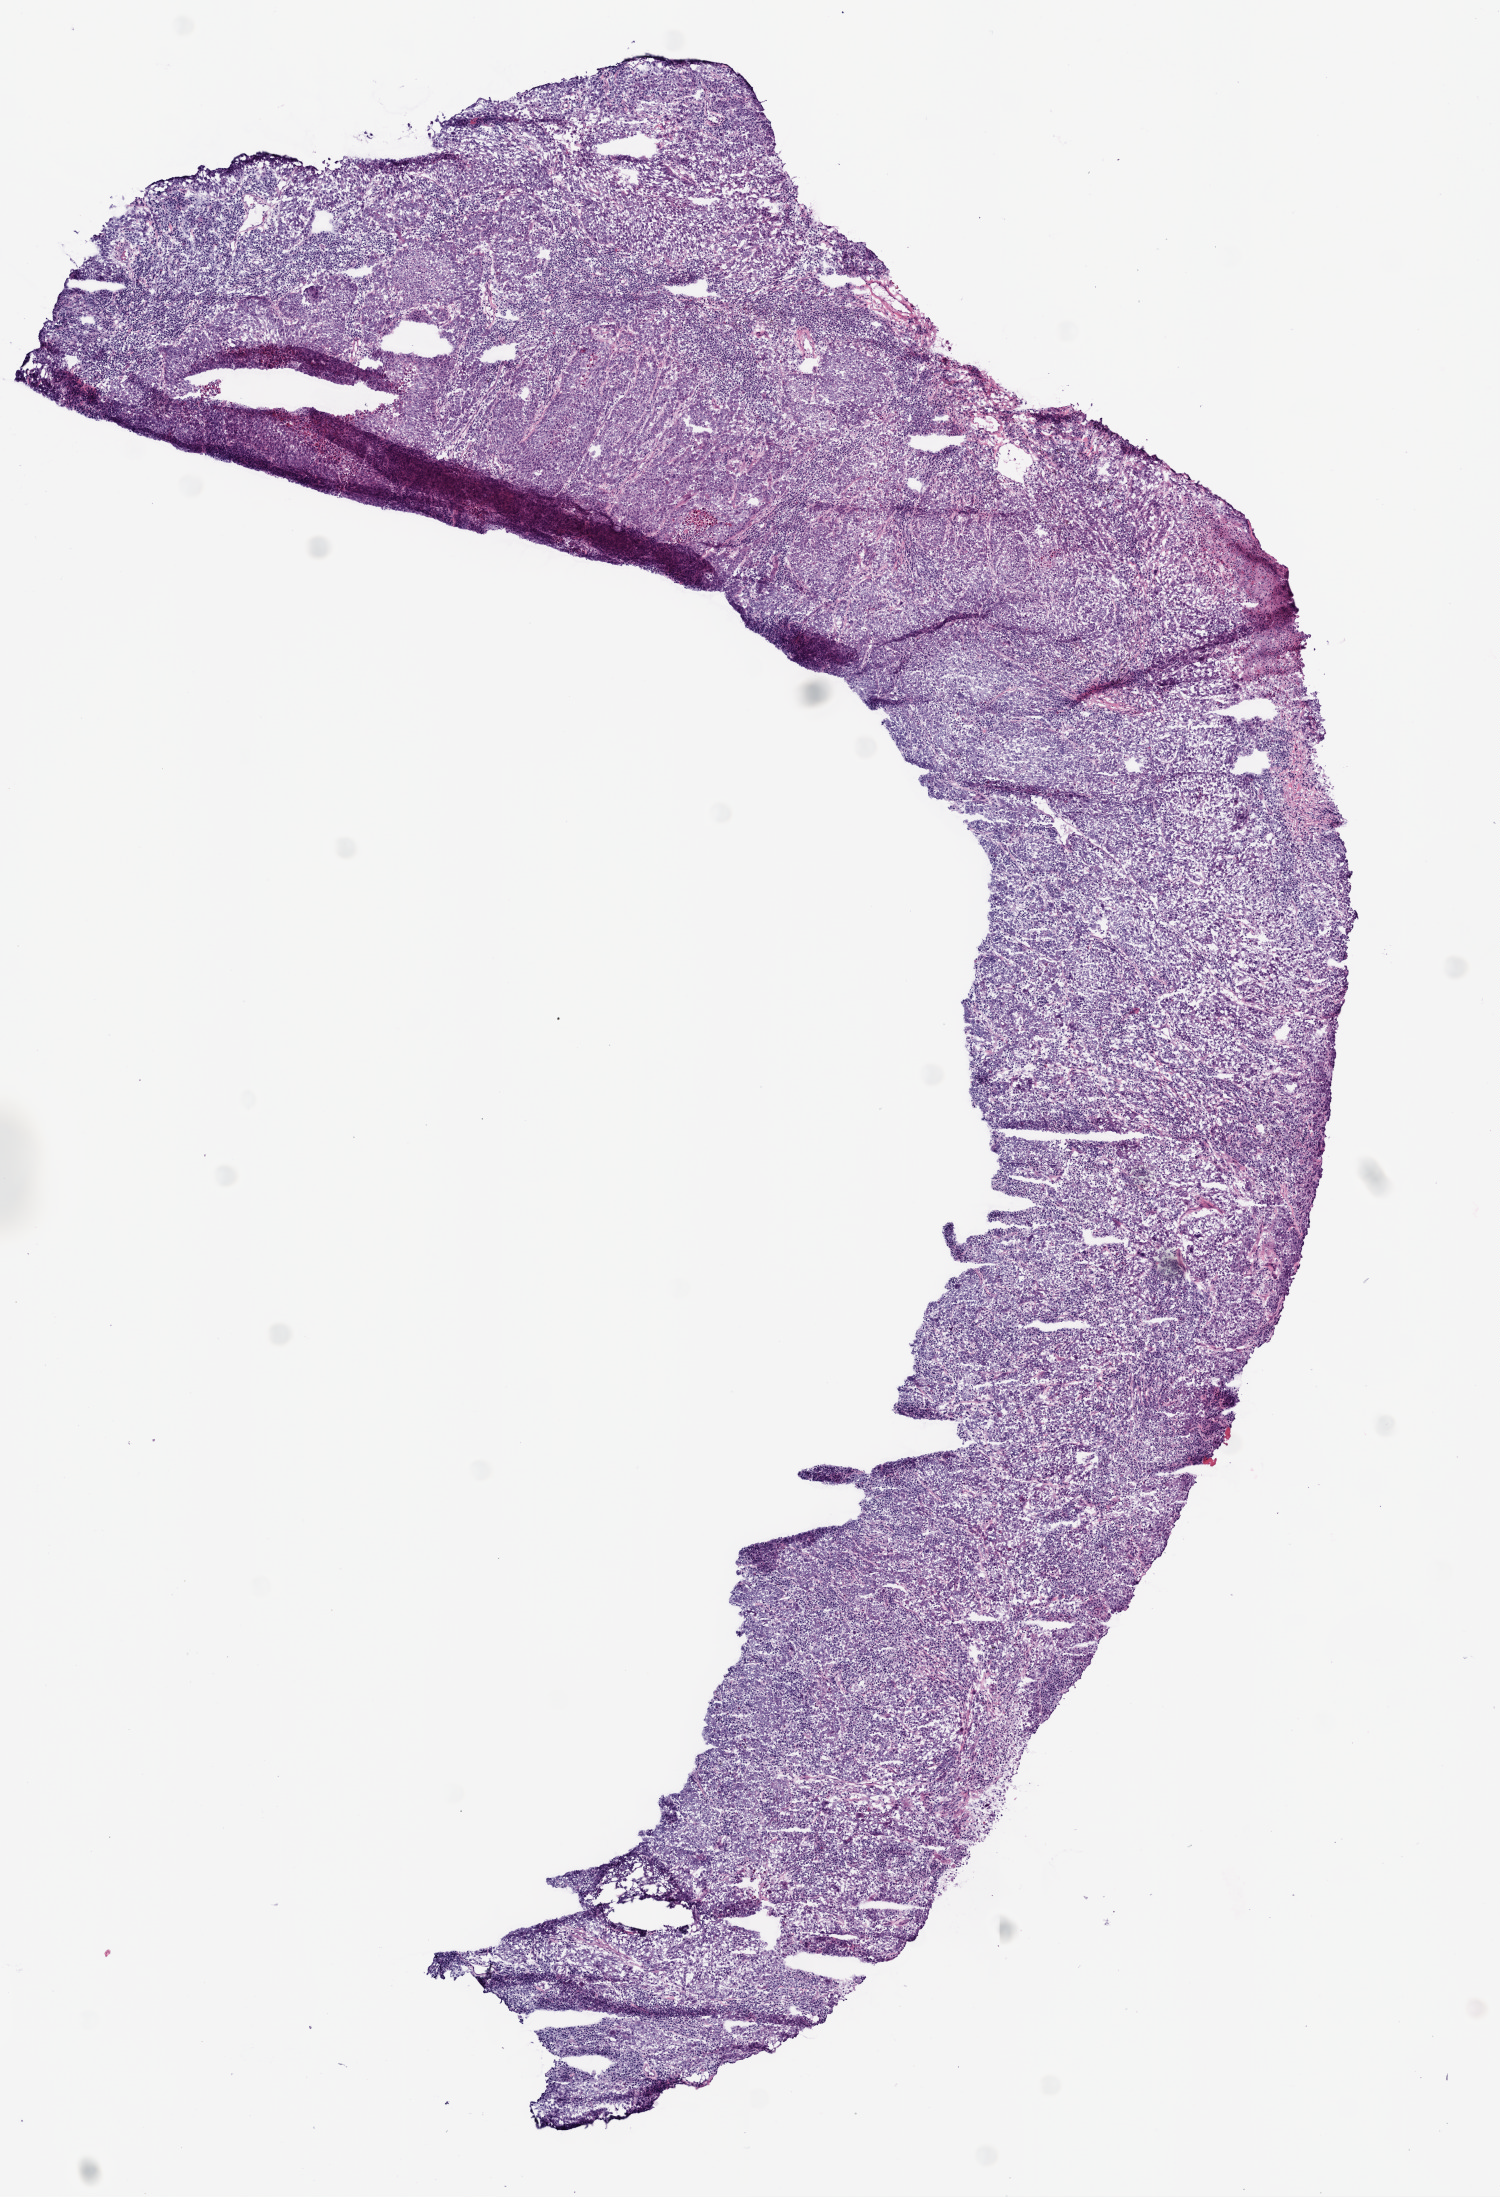
Digitized H&E-stained tissue section (whole slide) — whole scanned area (about 6.0 x 8.8 mm, slide scanned at 20x) shown as a low-resolution overview; frozen section from the bottom of the tissue portion; lung, primary tumour sample. Male patient; age at initial diagnosis 73 years. Slide review estimates, as recorded: tumour nuclei 75%, necrosis 0%. Inflammatory infiltration, as recorded: lymphocyte infiltration 27%, monocyte infiltration 2%, neutrophil infiltration 2%.
* laterality: left
* AJCC pathologic stage: IIB
* histologic diagnosis: Squamous cell carcinoma, NOS